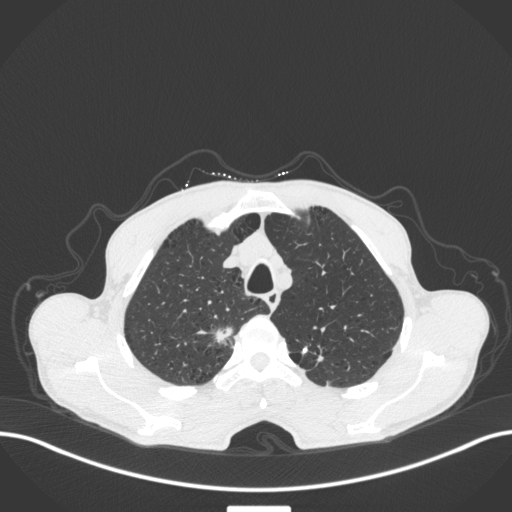
Chest CT, one axial slice. Position 351 of 445 along the scan axis. Reconstruction kernel B31f. 120 kVp. Lung window (W 1500 / L -600 HU). 1 mm slice thickness. 512 × 512 image matrix. Male patient, age 70 years. From the clinical record (not read from this slice): clinical TNM (as recorded): T1a N0 M0.
Annotated regions visible in this slice (rectangle marked by the reading radiologist):
- lung tumour (recorded histology: adenocarcinoma): bounding box <197,325,237,352> (left, top, right, bottom; pixels)